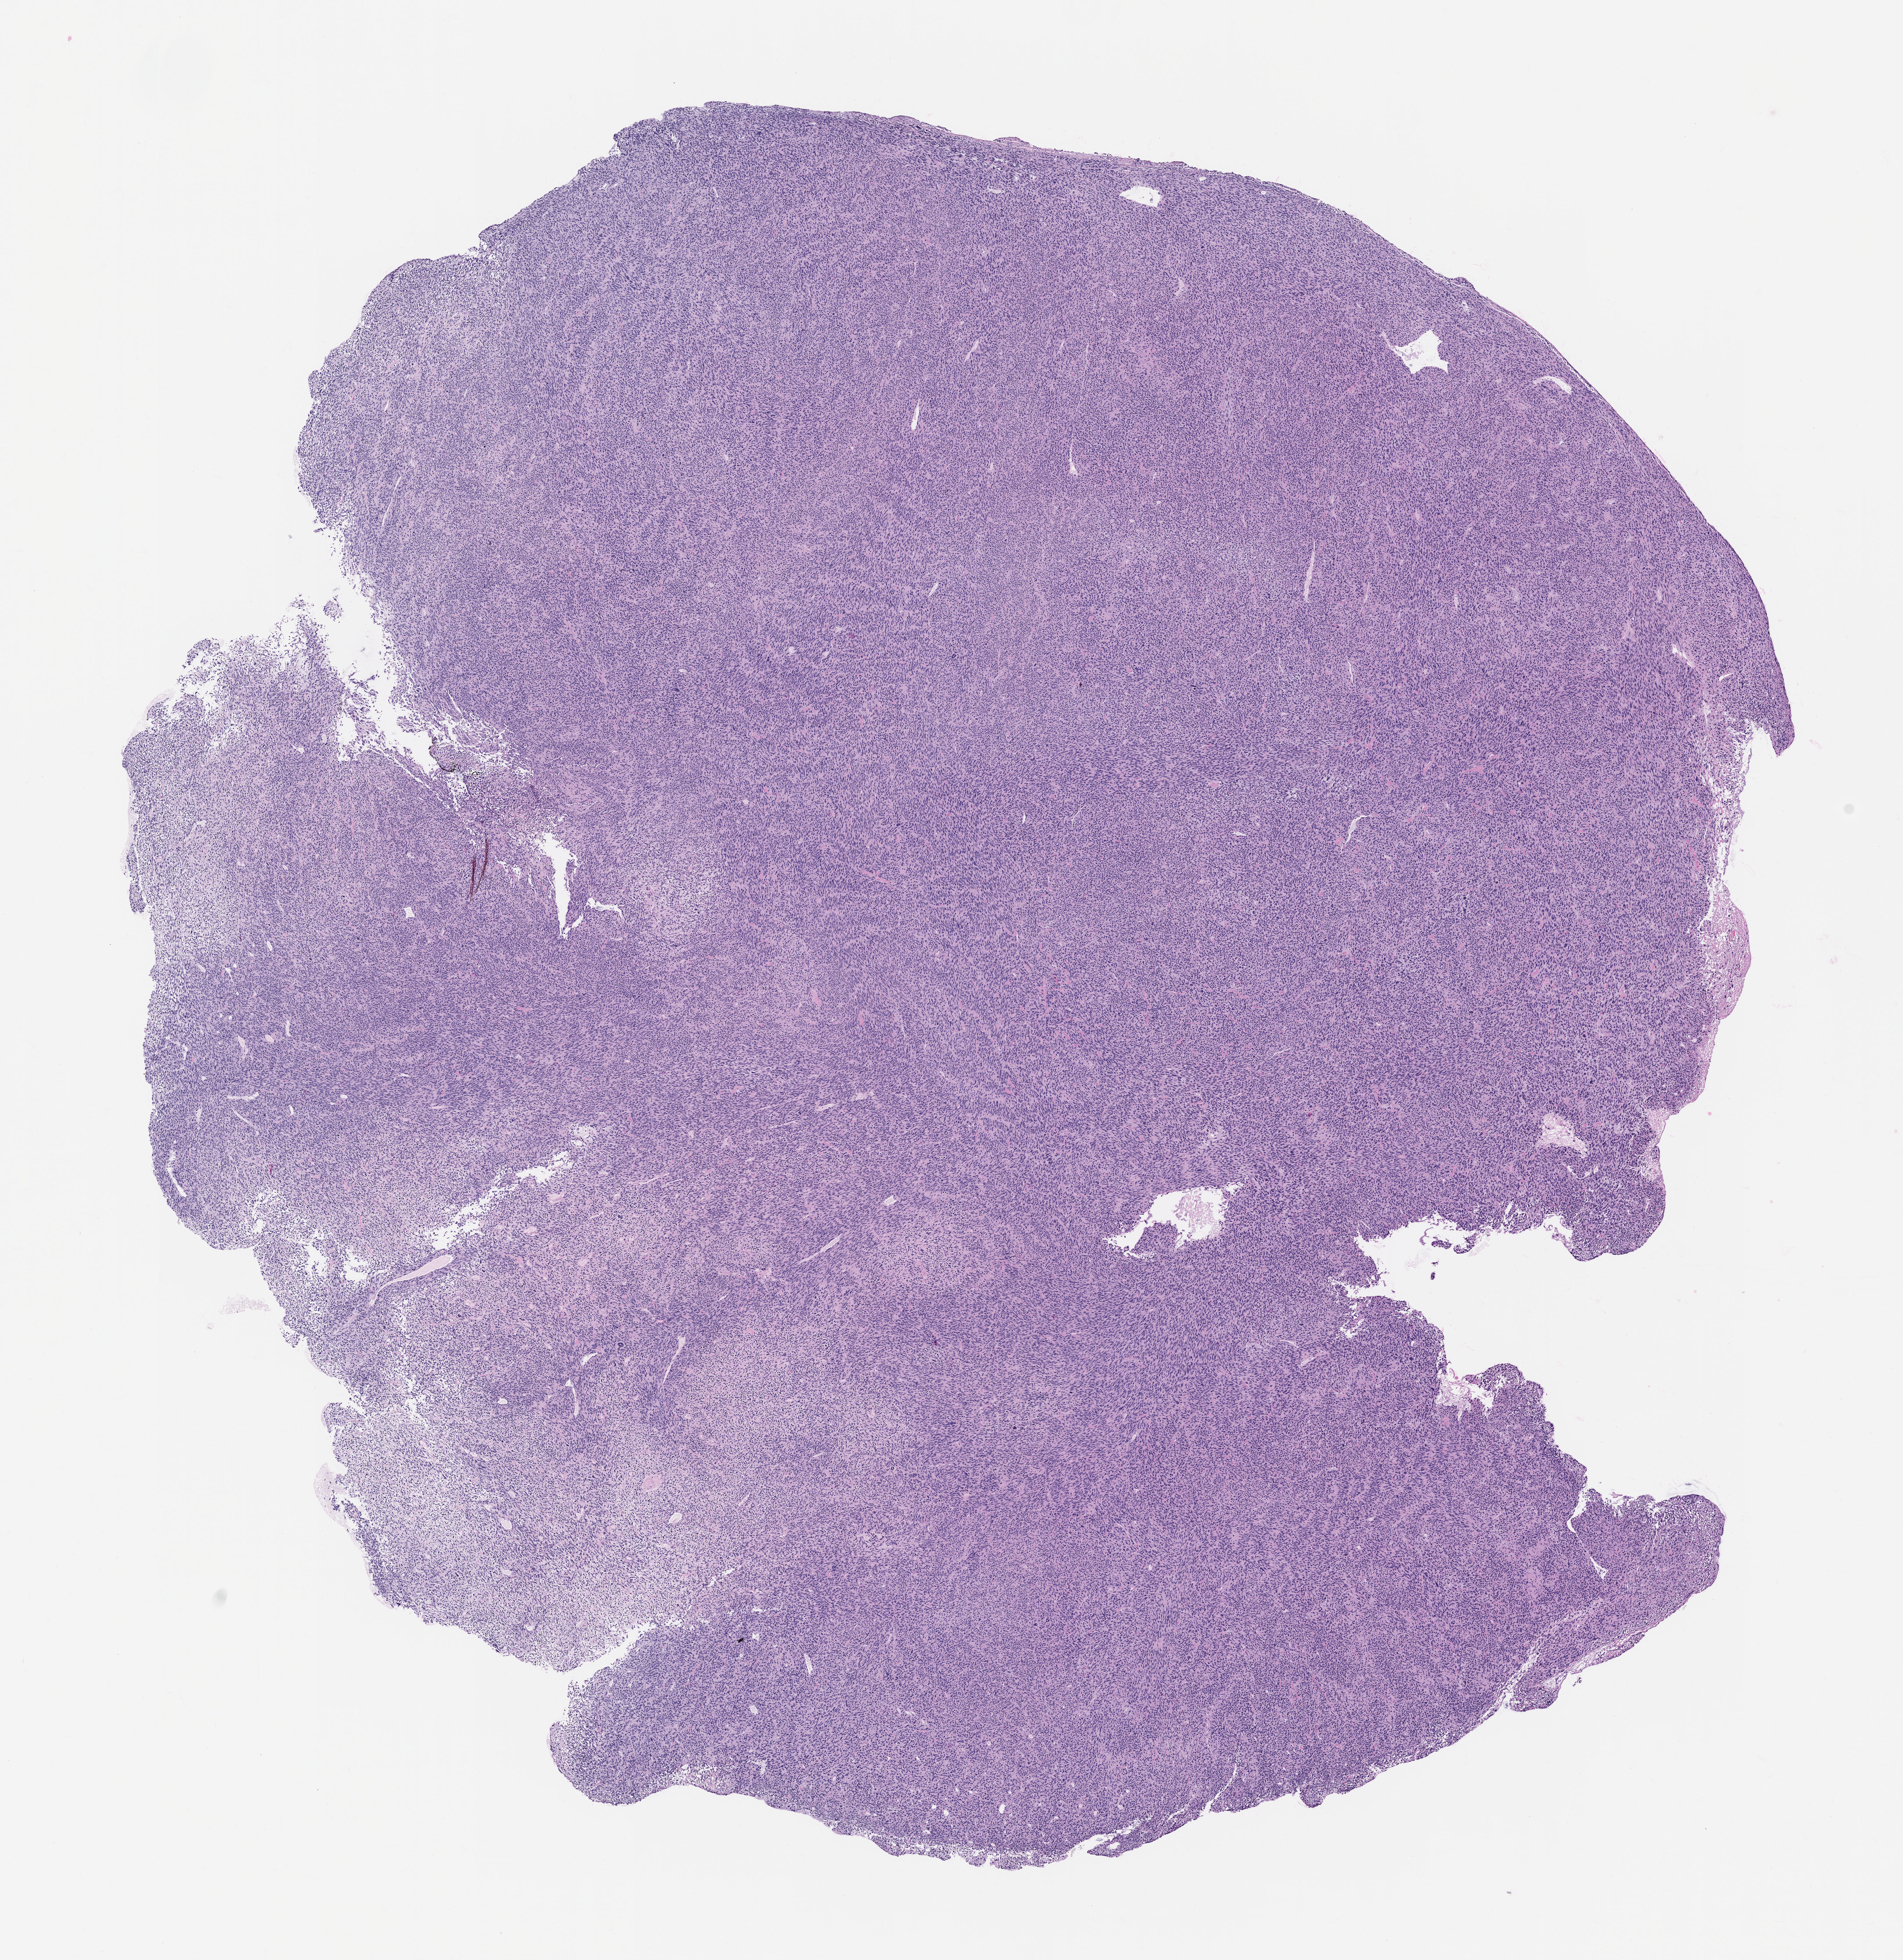
H&E whole-slide image of a patient-derived xenograft (PDX) tumor grown in a mouse, passage 2 — a low-resolution overview of the entire scanned area, about 12.0 x 12.4 mm, FFPE section, originating tumor site category: uterus.
* originating patient diagnosis: Leiomyosarcoma